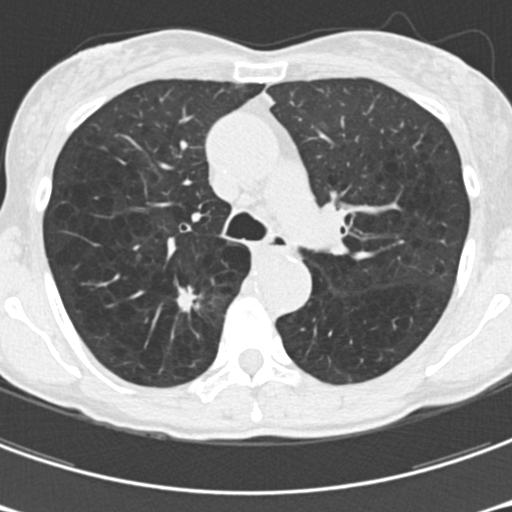
Low-dose screening chest CT, axial slice, third screening round (two years after baseline), lung window (W 1500 / L -600 HU), slice 62 of 176 in the series. Female participant, aged 61 years at enrolment. Current smoker at enrolment.
Expert reader's lesion annotation, bounding box <162,275,221,331> (left, top, right, bottom; pixels). The screening reader recorded 2 non-calcified nodules or masses ≥4 mm on this exam; which of them this box marks is not recorded.